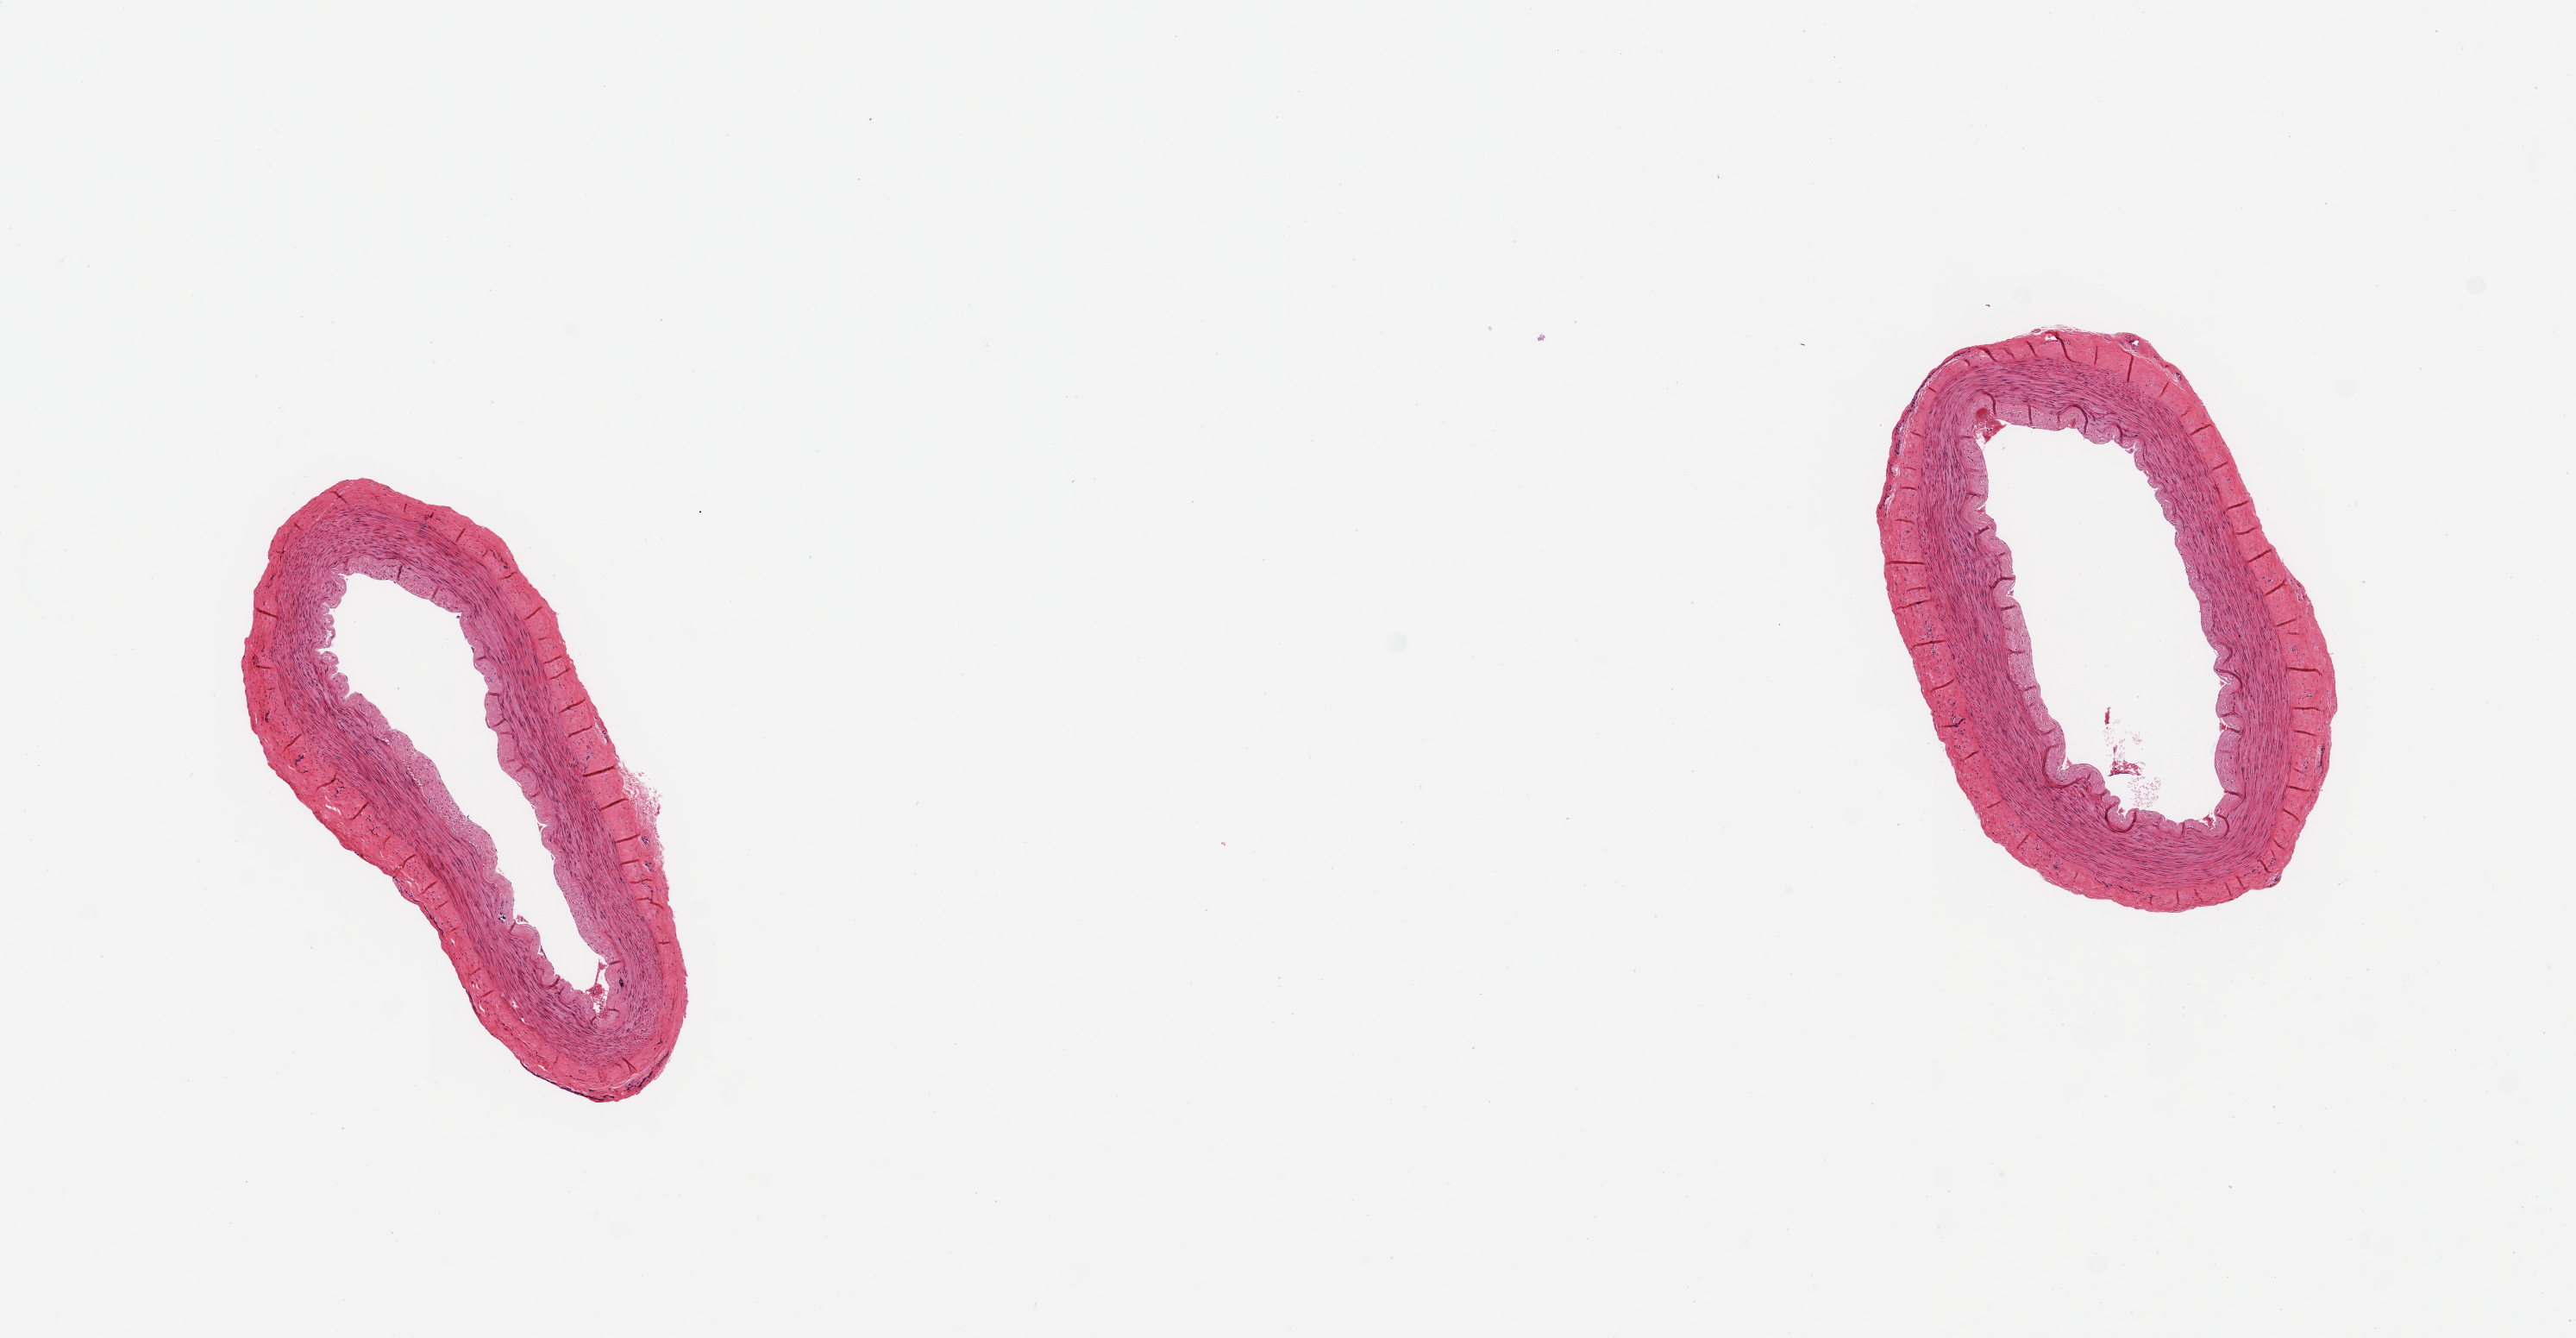
Whole-slide image, haematoxylin and eosin stain, whole scanned area (about 11.8 x 6.1 mm) shown as a low-resolution overview; PAXgene-fixed, paraffin-embedded tissue; section of tibial artery (target tissue); donor tissue sample.
Reviewer comment on this tissue sample: 2 pieces; minimal fibrous intimal thickening; no plaques; well trimmed.